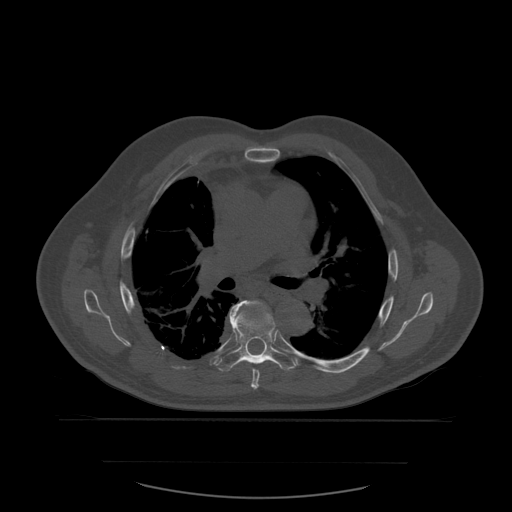
CT including the spine, one axial slice. Slice 391 of 590 in the series (ordered by position). Bone window (W 1800 / L 400 HU). 512 × 512 image matrix. Patient age 71 years. Case-level facts recorded for this patient, not image findings: primary cancer: lung.
Structures marked on this image (semi-automatically segmented with operator editing):
- T6 vertebra: box from (x=239, y=301) to (x=268, y=390) px
- T7 vertebra: (x=217, y=302)–(x=298, y=372)